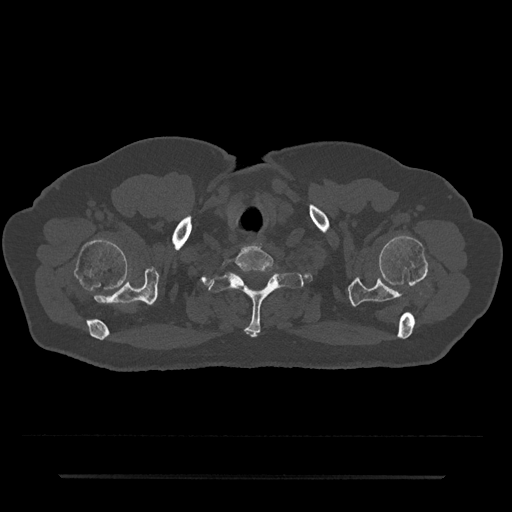
CT including the spine, one axial slice; slice 651 of 797 in the series (ordered by position); reconstruction kernel Br40s/3; 120 kVp; bone window (W 1800 / L 400 HU); 0.5 mm slice thickness; 512 × 512 image matrix, field of view 437 × 437 mm. Male patient, age 69 years. Case-level facts recorded for this patient, not image findings: primary cancer: prostate.
Outlined on this slice (semi-automatically segmented with operator editing):
- T1 vertebra: box from (x=208, y=269) to (x=304, y=336) px